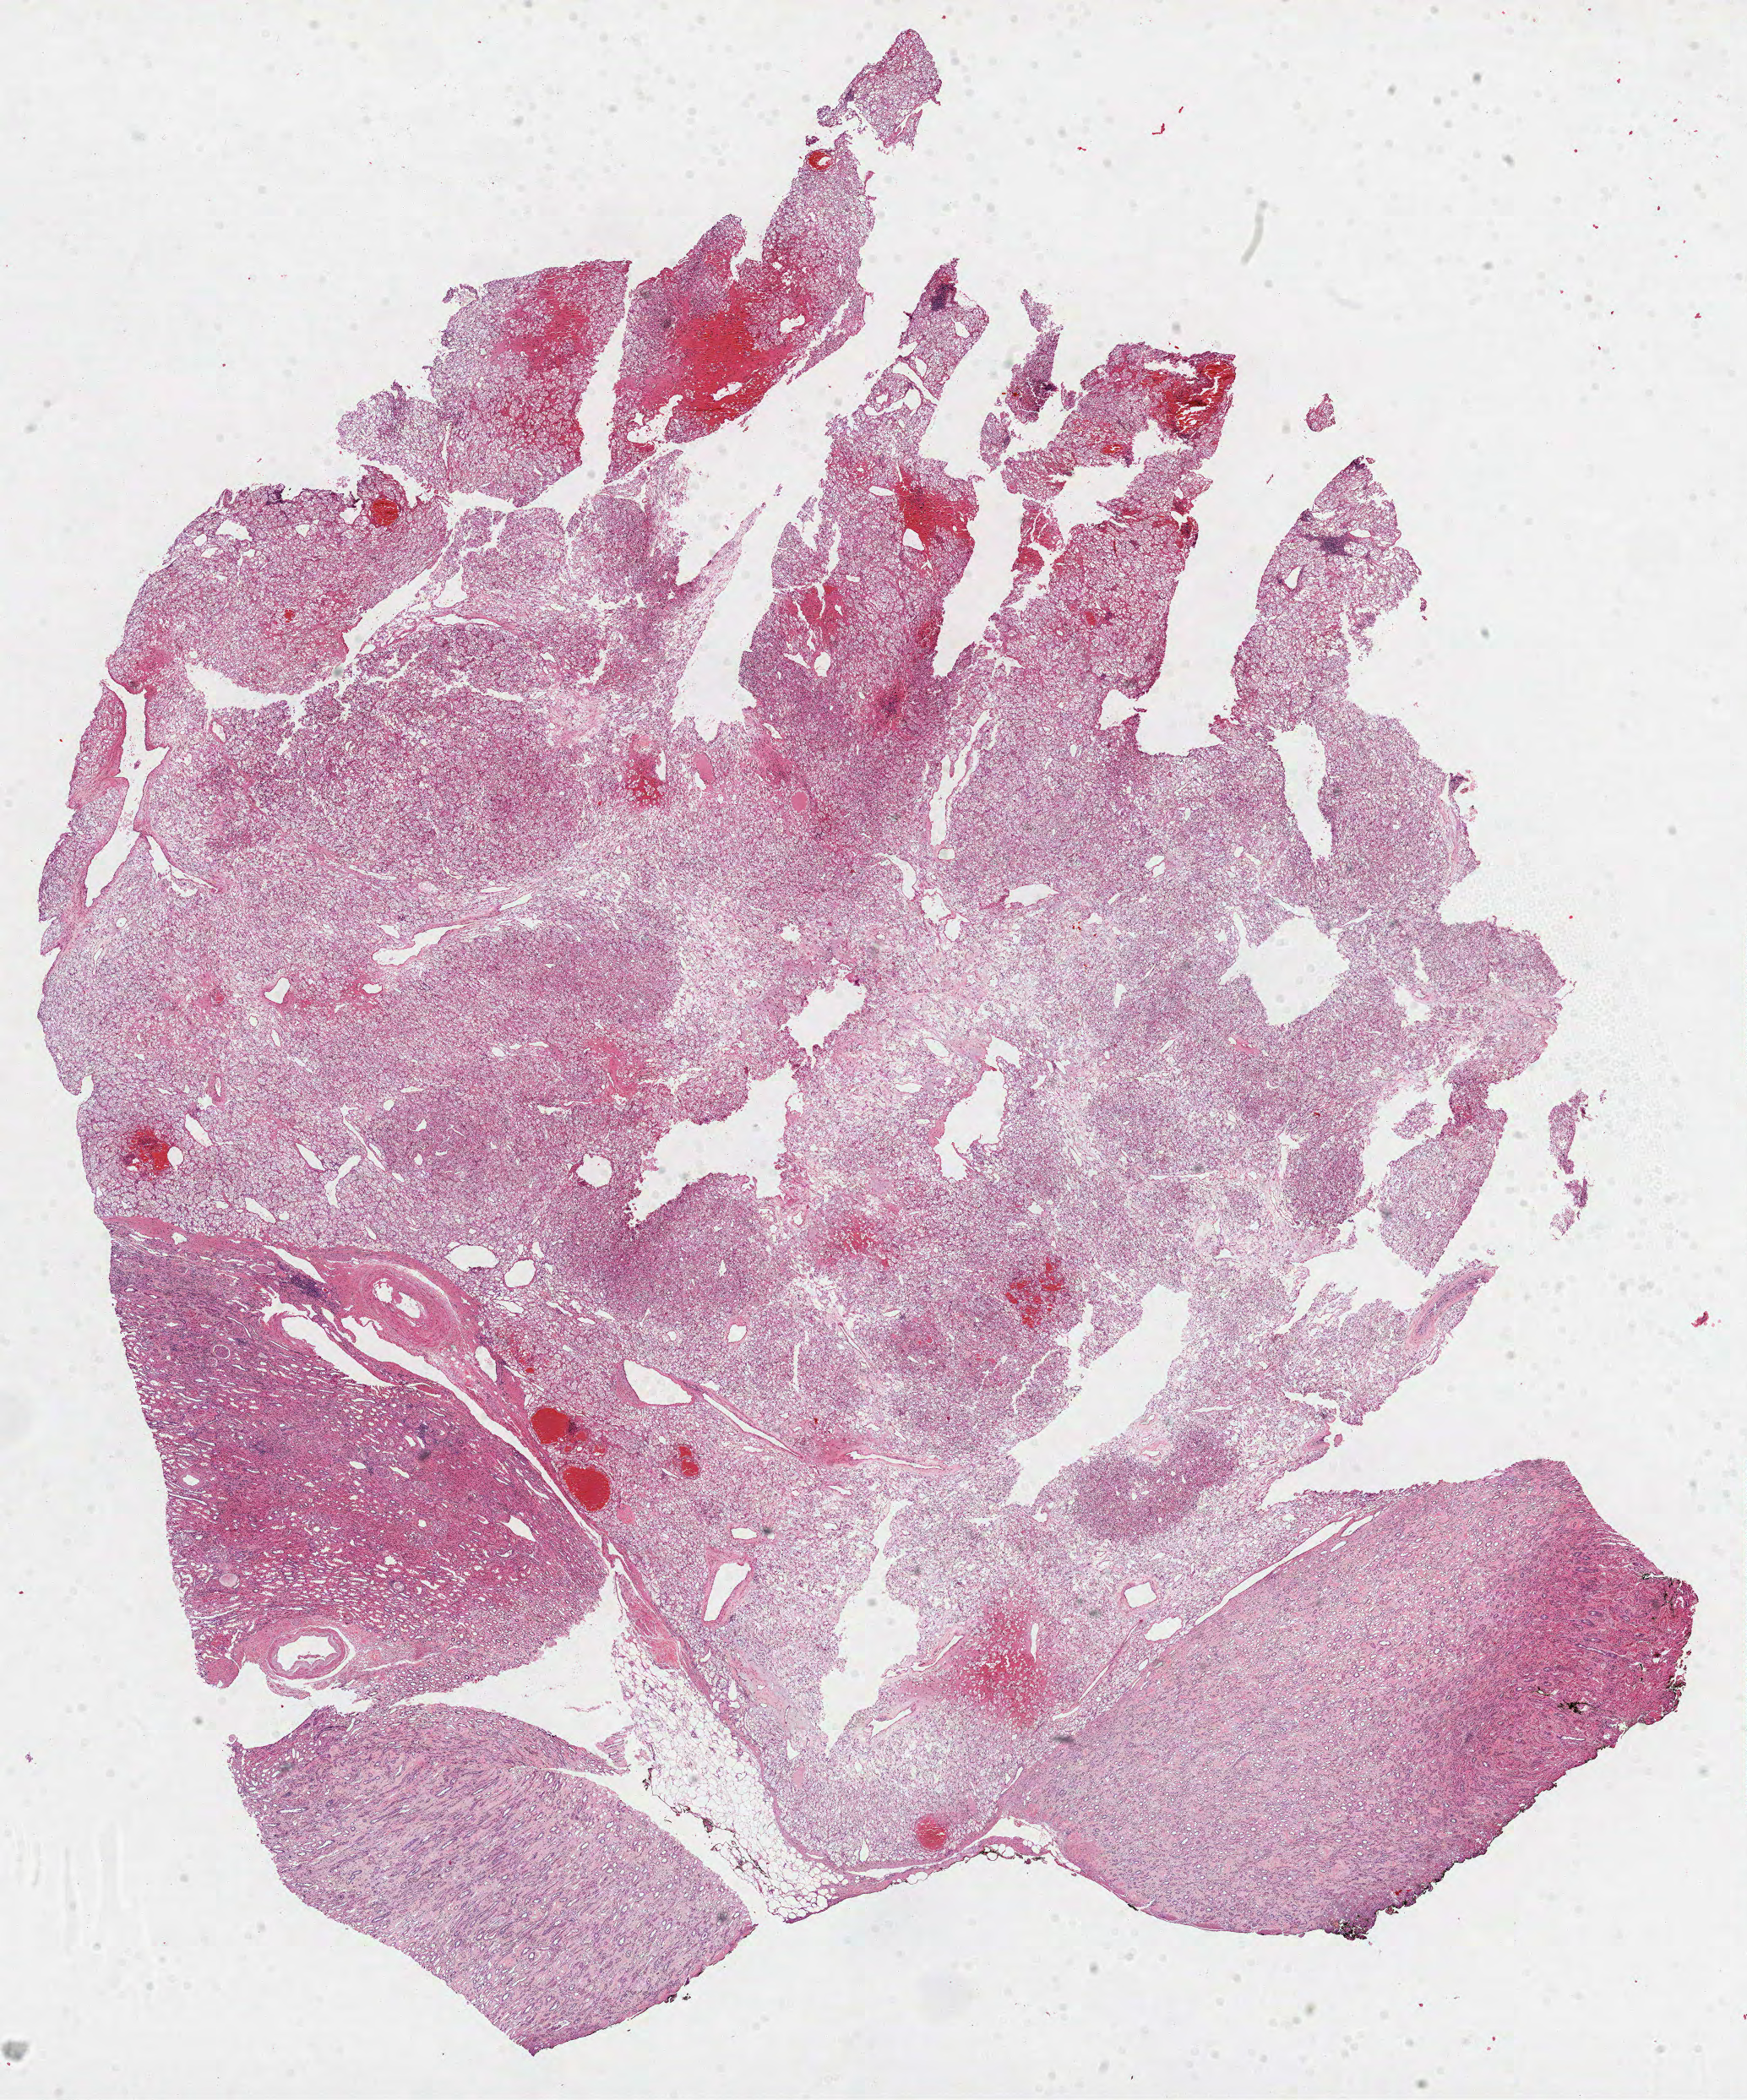
Hematoxylin and eosin (H&E) stained whole-slide image, whole scanned area (about 16.7 x 20.1 mm, slide scanned at 40x) shown as a low-resolution overview; formalin-fixed paraffin-embedded (FFPE) diagnostic section; sample: primary tumour, kidney. Patient: male, age at initial diagnosis 77 years. Histologic grade: G2 (moderately differentiated).
- AJCC pathologic stage: I (6th edition)
- pathologic diagnosis: Clear cell adenocarcinoma, NOS